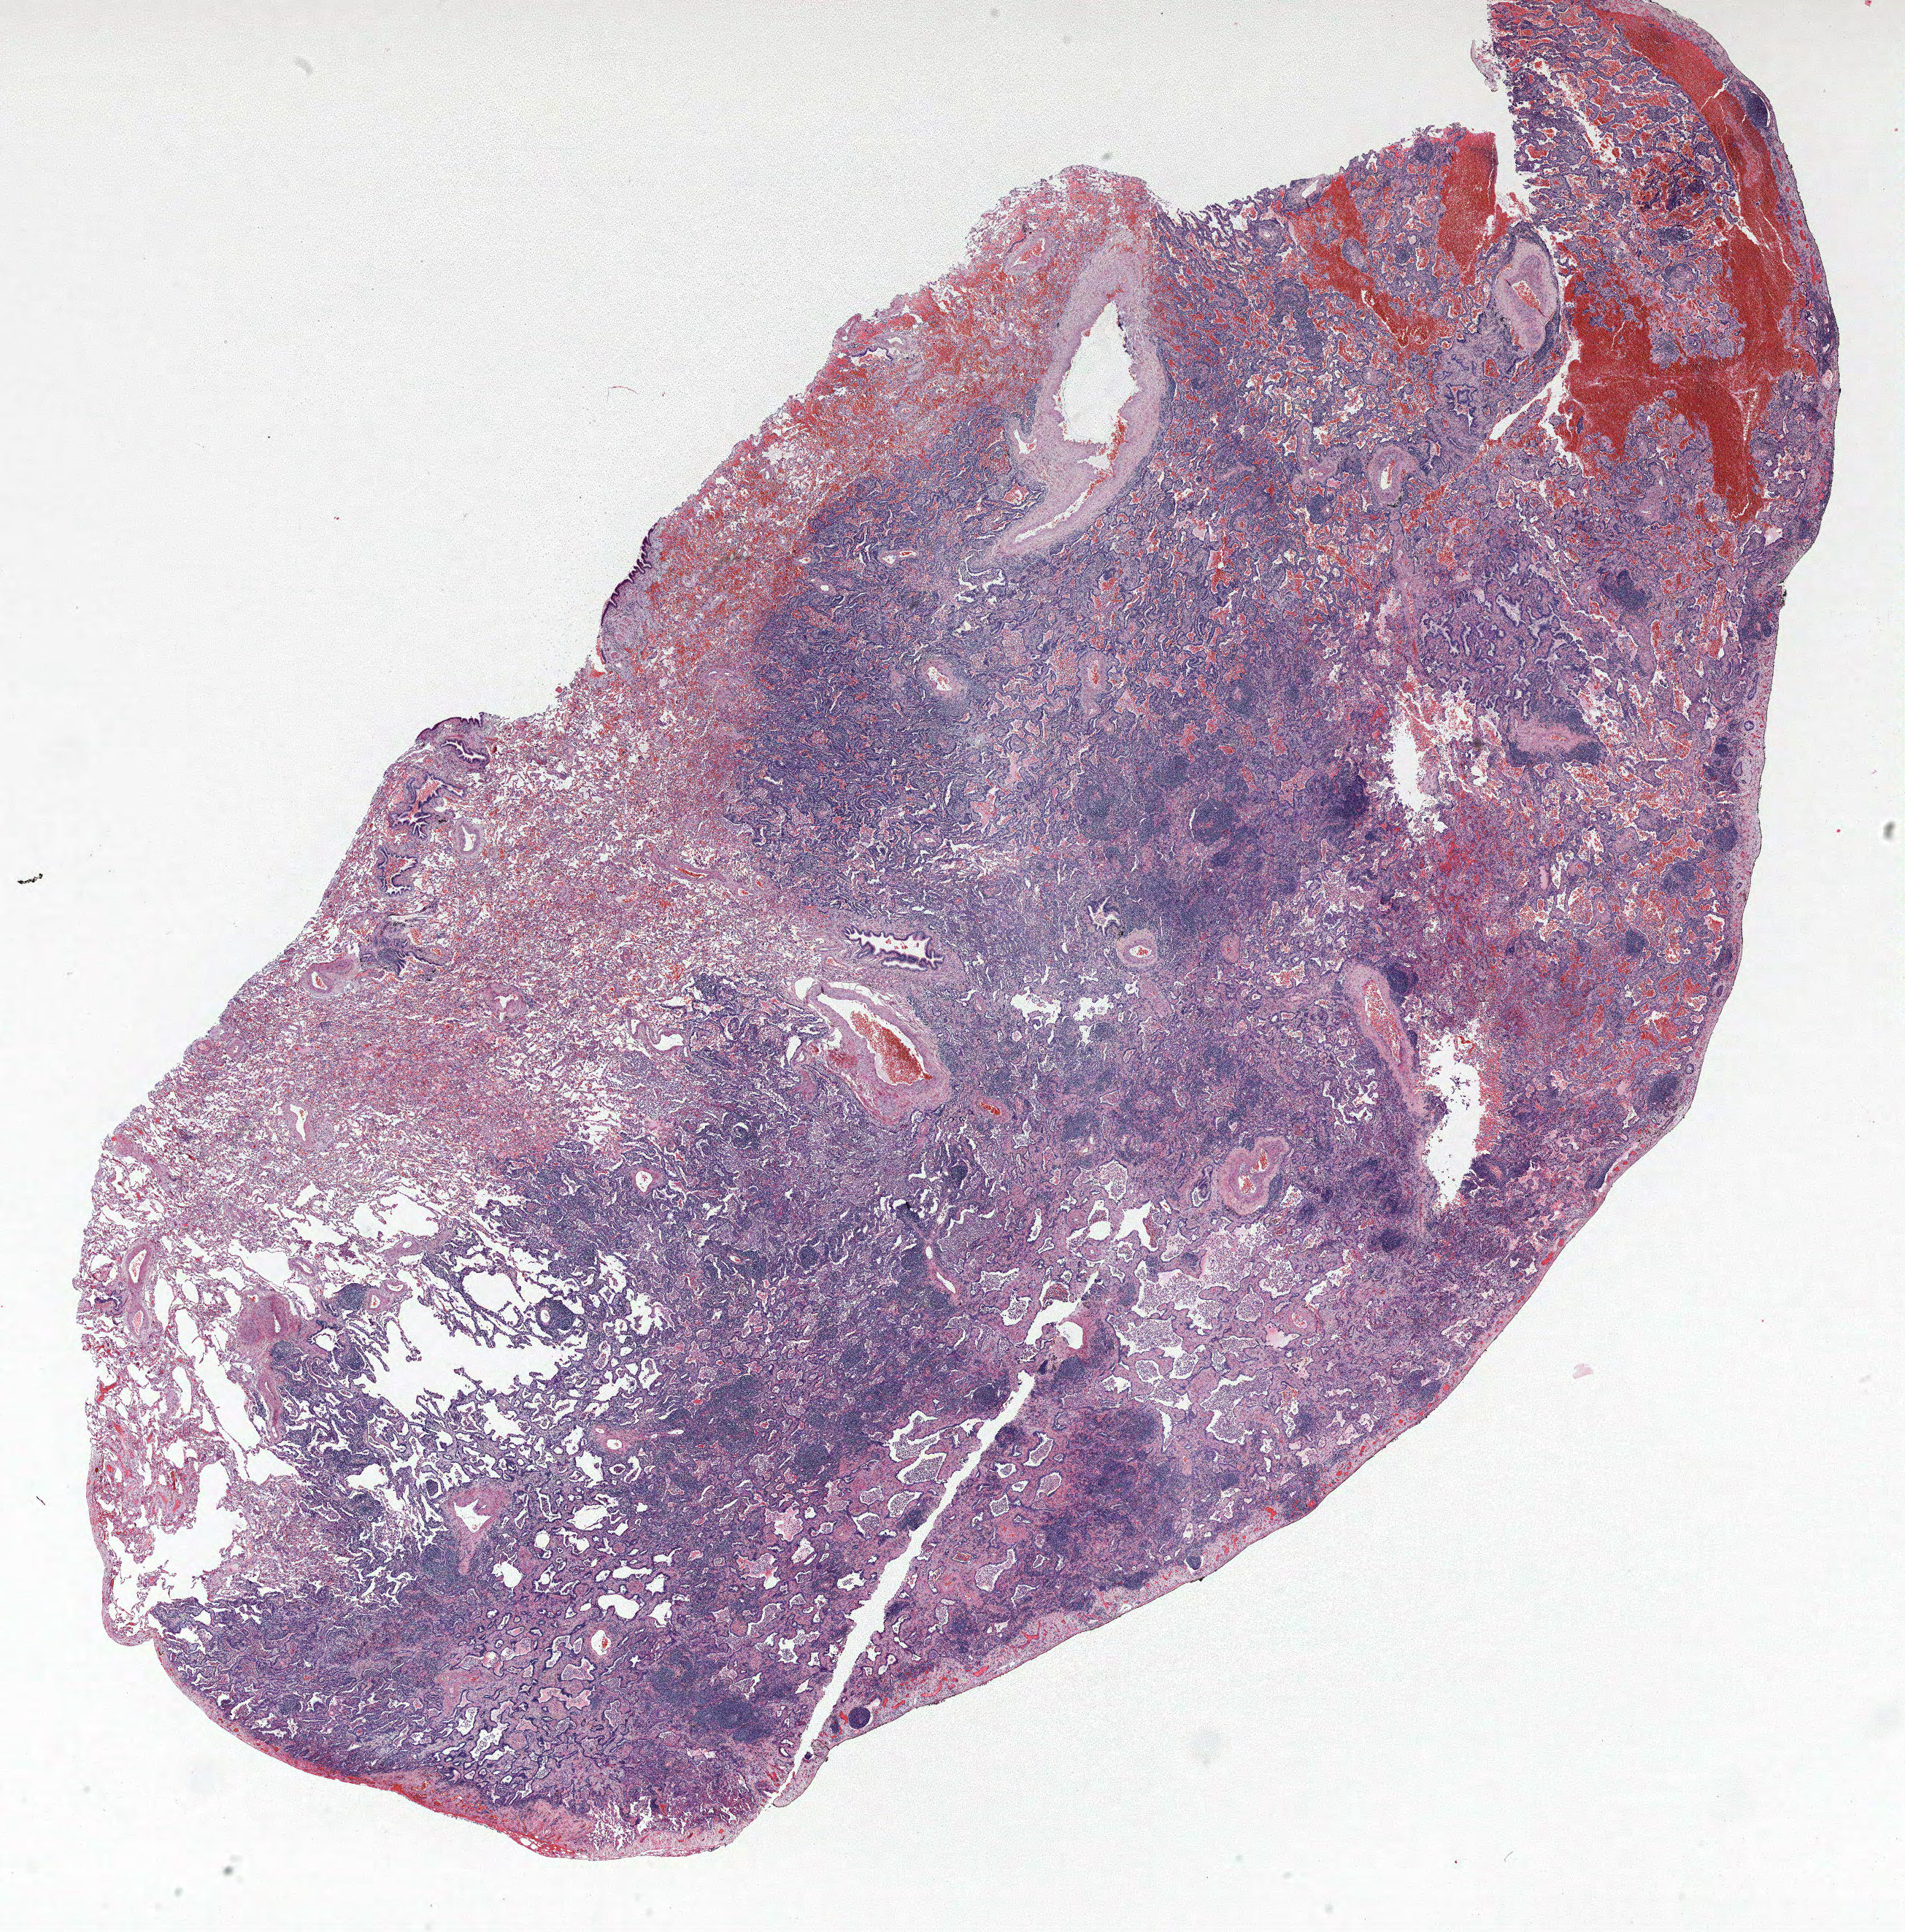
Whole-slide histology image, H&E — a low-resolution overview of the entire scanned area, about 20.9 x 21.2 mm (slide scanned at 40x), formalin-fixed paraffin-embedded (FFPE) section, lung. Male, age 61 at enrolment. Former smoker at enrolment.
Tumour size (pathology): 21 mm. Primary tumour location (clinical record): right lower lobe. Participant's lung-cancer diagnosis: Bronchiolo-alveolar adenocarcinoma, NOS (ICD-O-3 8250/3). Stage (AJCC 6th edition): IA.